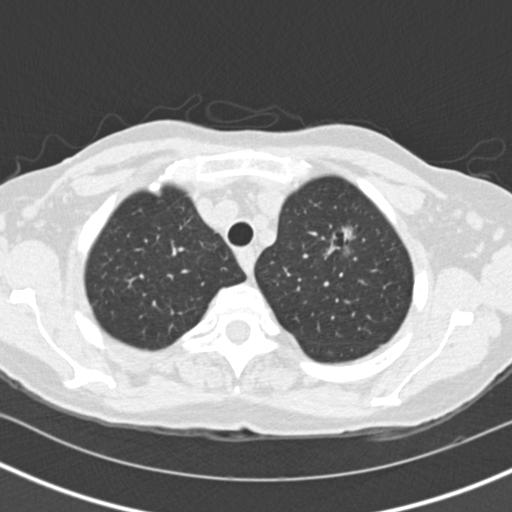
Axial slice from a low-dose chest CT screening exam. Baseline annual screen. Lung window (W 1500 / L -600 HU). 2 mm slice thickness. Female participant, aged 73 years at enrolment. Current smoker at enrolment.
Expert reader's lesion annotation, bounding box <312,218,365,281> (left, top, right, bottom; pixels). Reader record for this screening exam (exam-level; its link to the box is not recorded): non-calcified nodule or mass ≥4 mm, left upper lobe, 27 × 21 mm, spiculated (stellate) margins, soft tissue attenuation. Official screen result: positive, change unspecified: nodule(s) >= 4 mm or enlarging nodule(s), mass(es), or other non-specific abnormalities suspicious for lung cancer. Participant outcome: lung cancer diagnosed 72 days after this screen — bronchiolo-alveolar adenocarcinoma, NOS, left upper lobe, moderately differentiated (G2), stage IIIB (AJCC 6th edition), 17 mm at pathology.